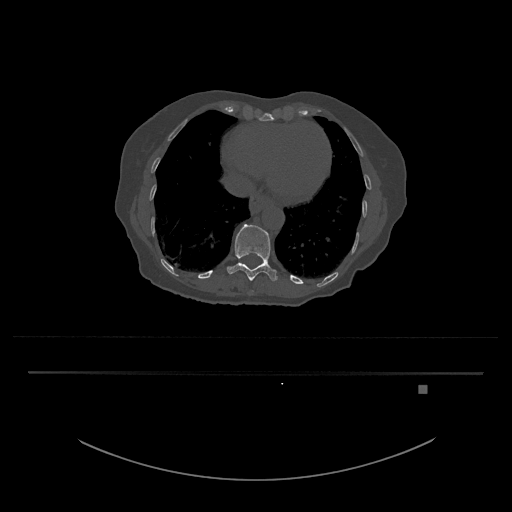
CT including the spine, one axial slice; reconstruction kernel Br40s/3; 120 kVp; bone window (W 1800 / L 400 HU); 0.5 mm slice thickness; 512 × 512 image matrix, field of view 500 × 500 mm. Female patient, age 57 years. From the clinical record (not read from this slice): primary cancer: cervical.
Structures marked on this image (semi-automatically segmented with operator editing):
- T11 vertebra: bounding box <227,224,278,281> (left, top, right, bottom; pixels)